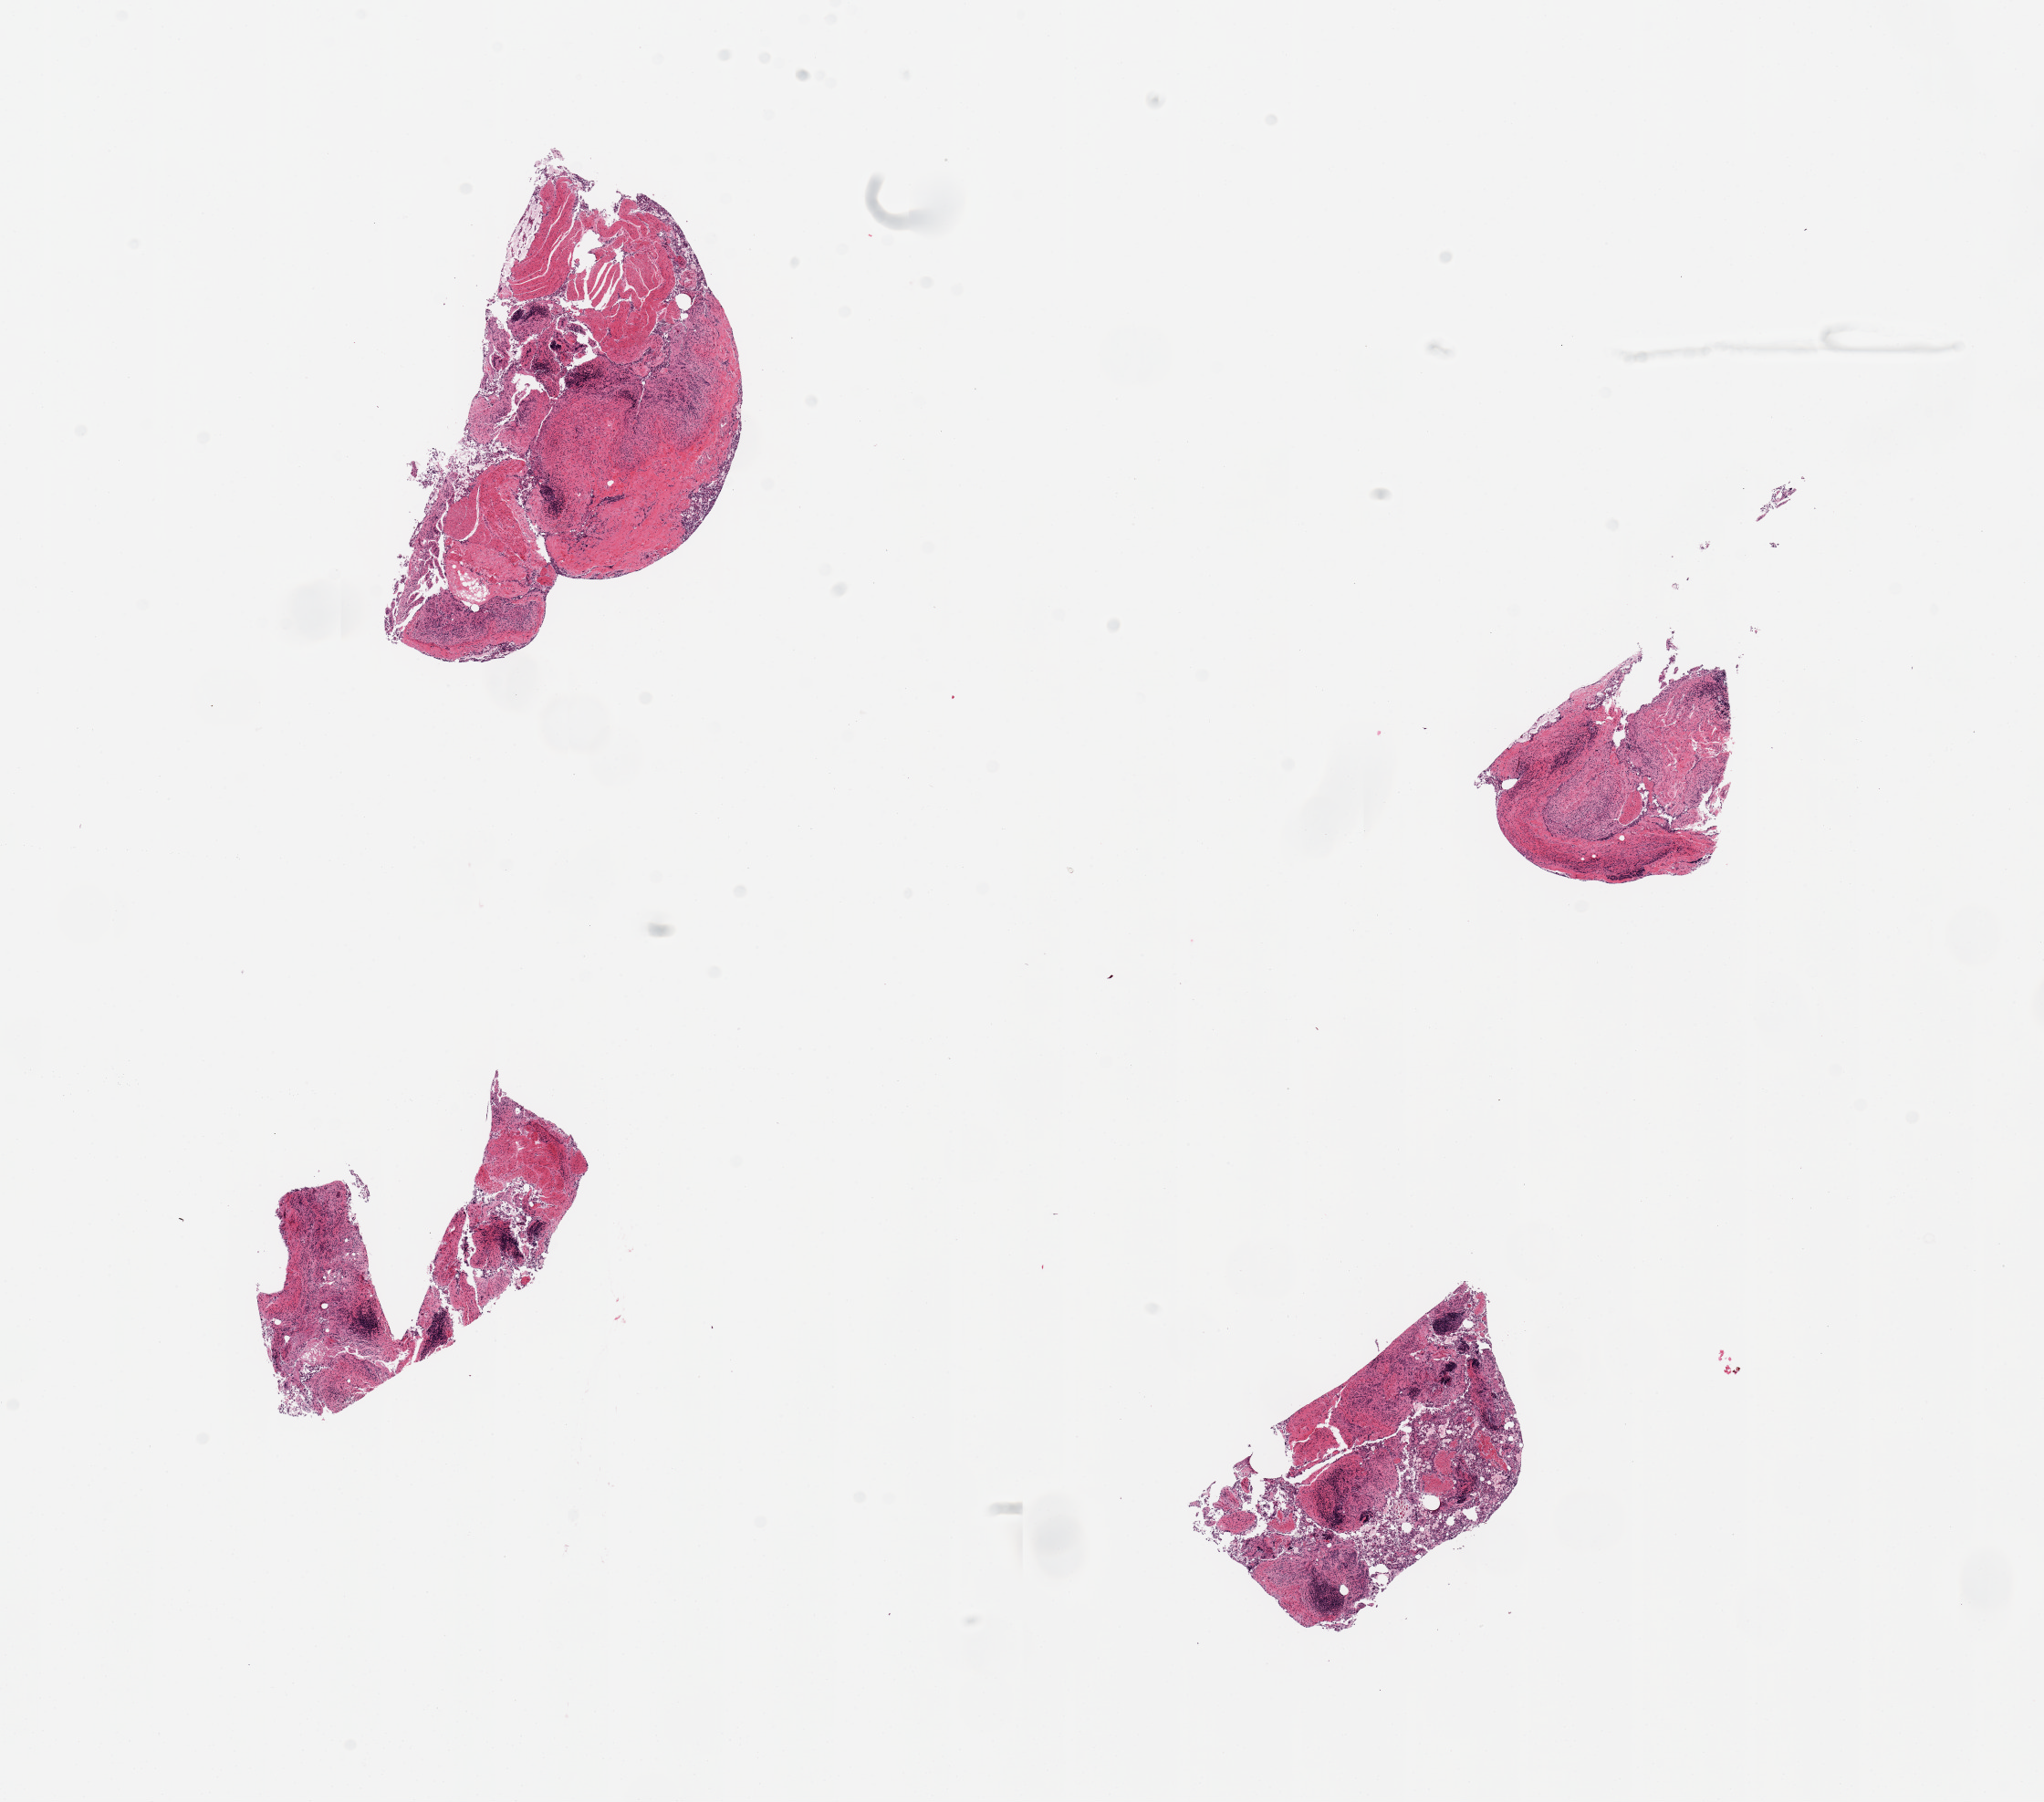
H&E whole-slide image — whole scanned area (about 17.7 x 15.6 mm, acquisition: 20x scan) shown as a low-resolution overview. Female donor.
- specimen: PAXgene-fixed, paraffin-embedded tissue; section of ileum (target tissue); tissue donor sample